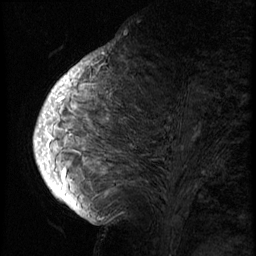
Breast MRI (dynamic contrast-enhanced), one sagittal slice. Position 30 of 74 along the scan axis. 3 images stored at this slice position (order not interpretable as contrast timing). 1.5 T. TE 4.2 ms, TR 8.9 ms. 2.5 mm slice thickness. 256 × 256 image matrix, field of view 200 × 200 mm. Patient: female, 57 years. From the clinical record (not read from this slice): setting: breast cancer imaged before/during neoadjuvant chemotherapy; receptor status: HER2-positive.
Structures marked on this image (semi-automatically segmented with operator editing):
- analysis volume of interest (the breast-tissue region the enhancement analysis was run in; not a lesion): bounding box [x1, y1, x2, y2] px = [40, 62, 233, 175]
- tumour enhancement mask (voxels above the 140 % enhancement threshold inside the analysis volume of interest): [45, 62, 93, 173]